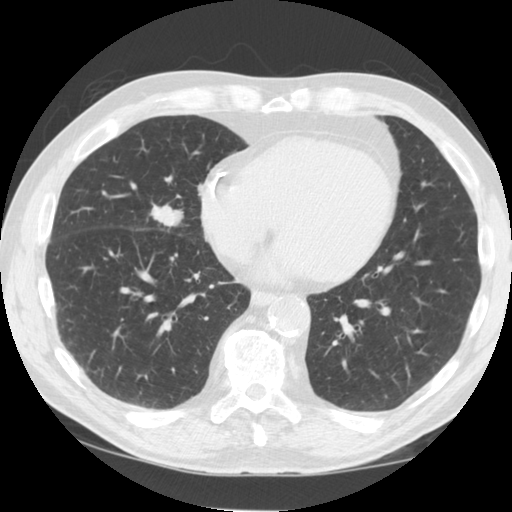
Low-dose screening chest CT, one axial slice. Slice 41 of 125 in the series (ordered by position). 120 kVp. Lung window (W 1500 / L -600 HU). 2.5 mm slice thickness. 512 × 512 image matrix.
Annotated regions visible in this slice (outlined manually by an expert reader):
- lesion 1 (tumor, middle lobe of right lung): bounding box <151,205,183,226> (left, top, right, bottom; pixels)